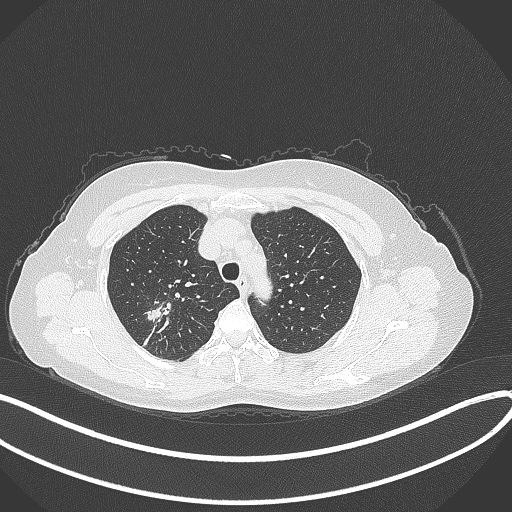
Chest CT, one axial slice; position 285 of 337 along the scan axis; reconstruction kernel B70f; 120 kVp; lung window (W 1500 / L -600 HU); 512 × 512 image matrix, field of view 400 × 400 mm. Patient: female, 50 years. Case-level facts recorded for this patient, not image findings: clinical TNM (as recorded): T1c N0 M0; histopathological grade: G2-3.
Structures marked on this image (rectangle marked by the reading radiologist):
- lung tumour (recorded histology: adenocarcinoma): bounding box (x1, y1, x2, y2) in pixels: (140, 299, 169, 323)